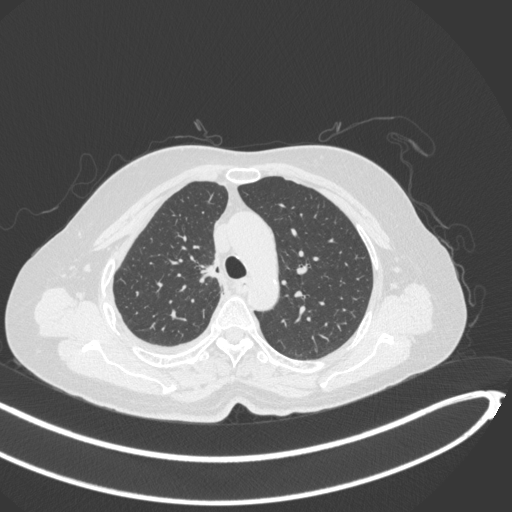
Chest CT, one axial slice; slice 221 of 297 in the series (ordered by position); reconstruction kernel B31f; 120 kVp; lung window (W 1500 / L -600 HU); 512 × 512 image matrix, field of view 400 × 400 mm. Patient: female, 64 years. From the clinical record (not read from this slice): clinical TNM (as recorded): T1b N0 M1.
Annotated regions visible in this slice (bounding box drawn by a radiologist):
- lung tumour (recorded histology: adenocarcinoma): bounding box [x1, y1, x2, y2] px = [198, 255, 223, 289]